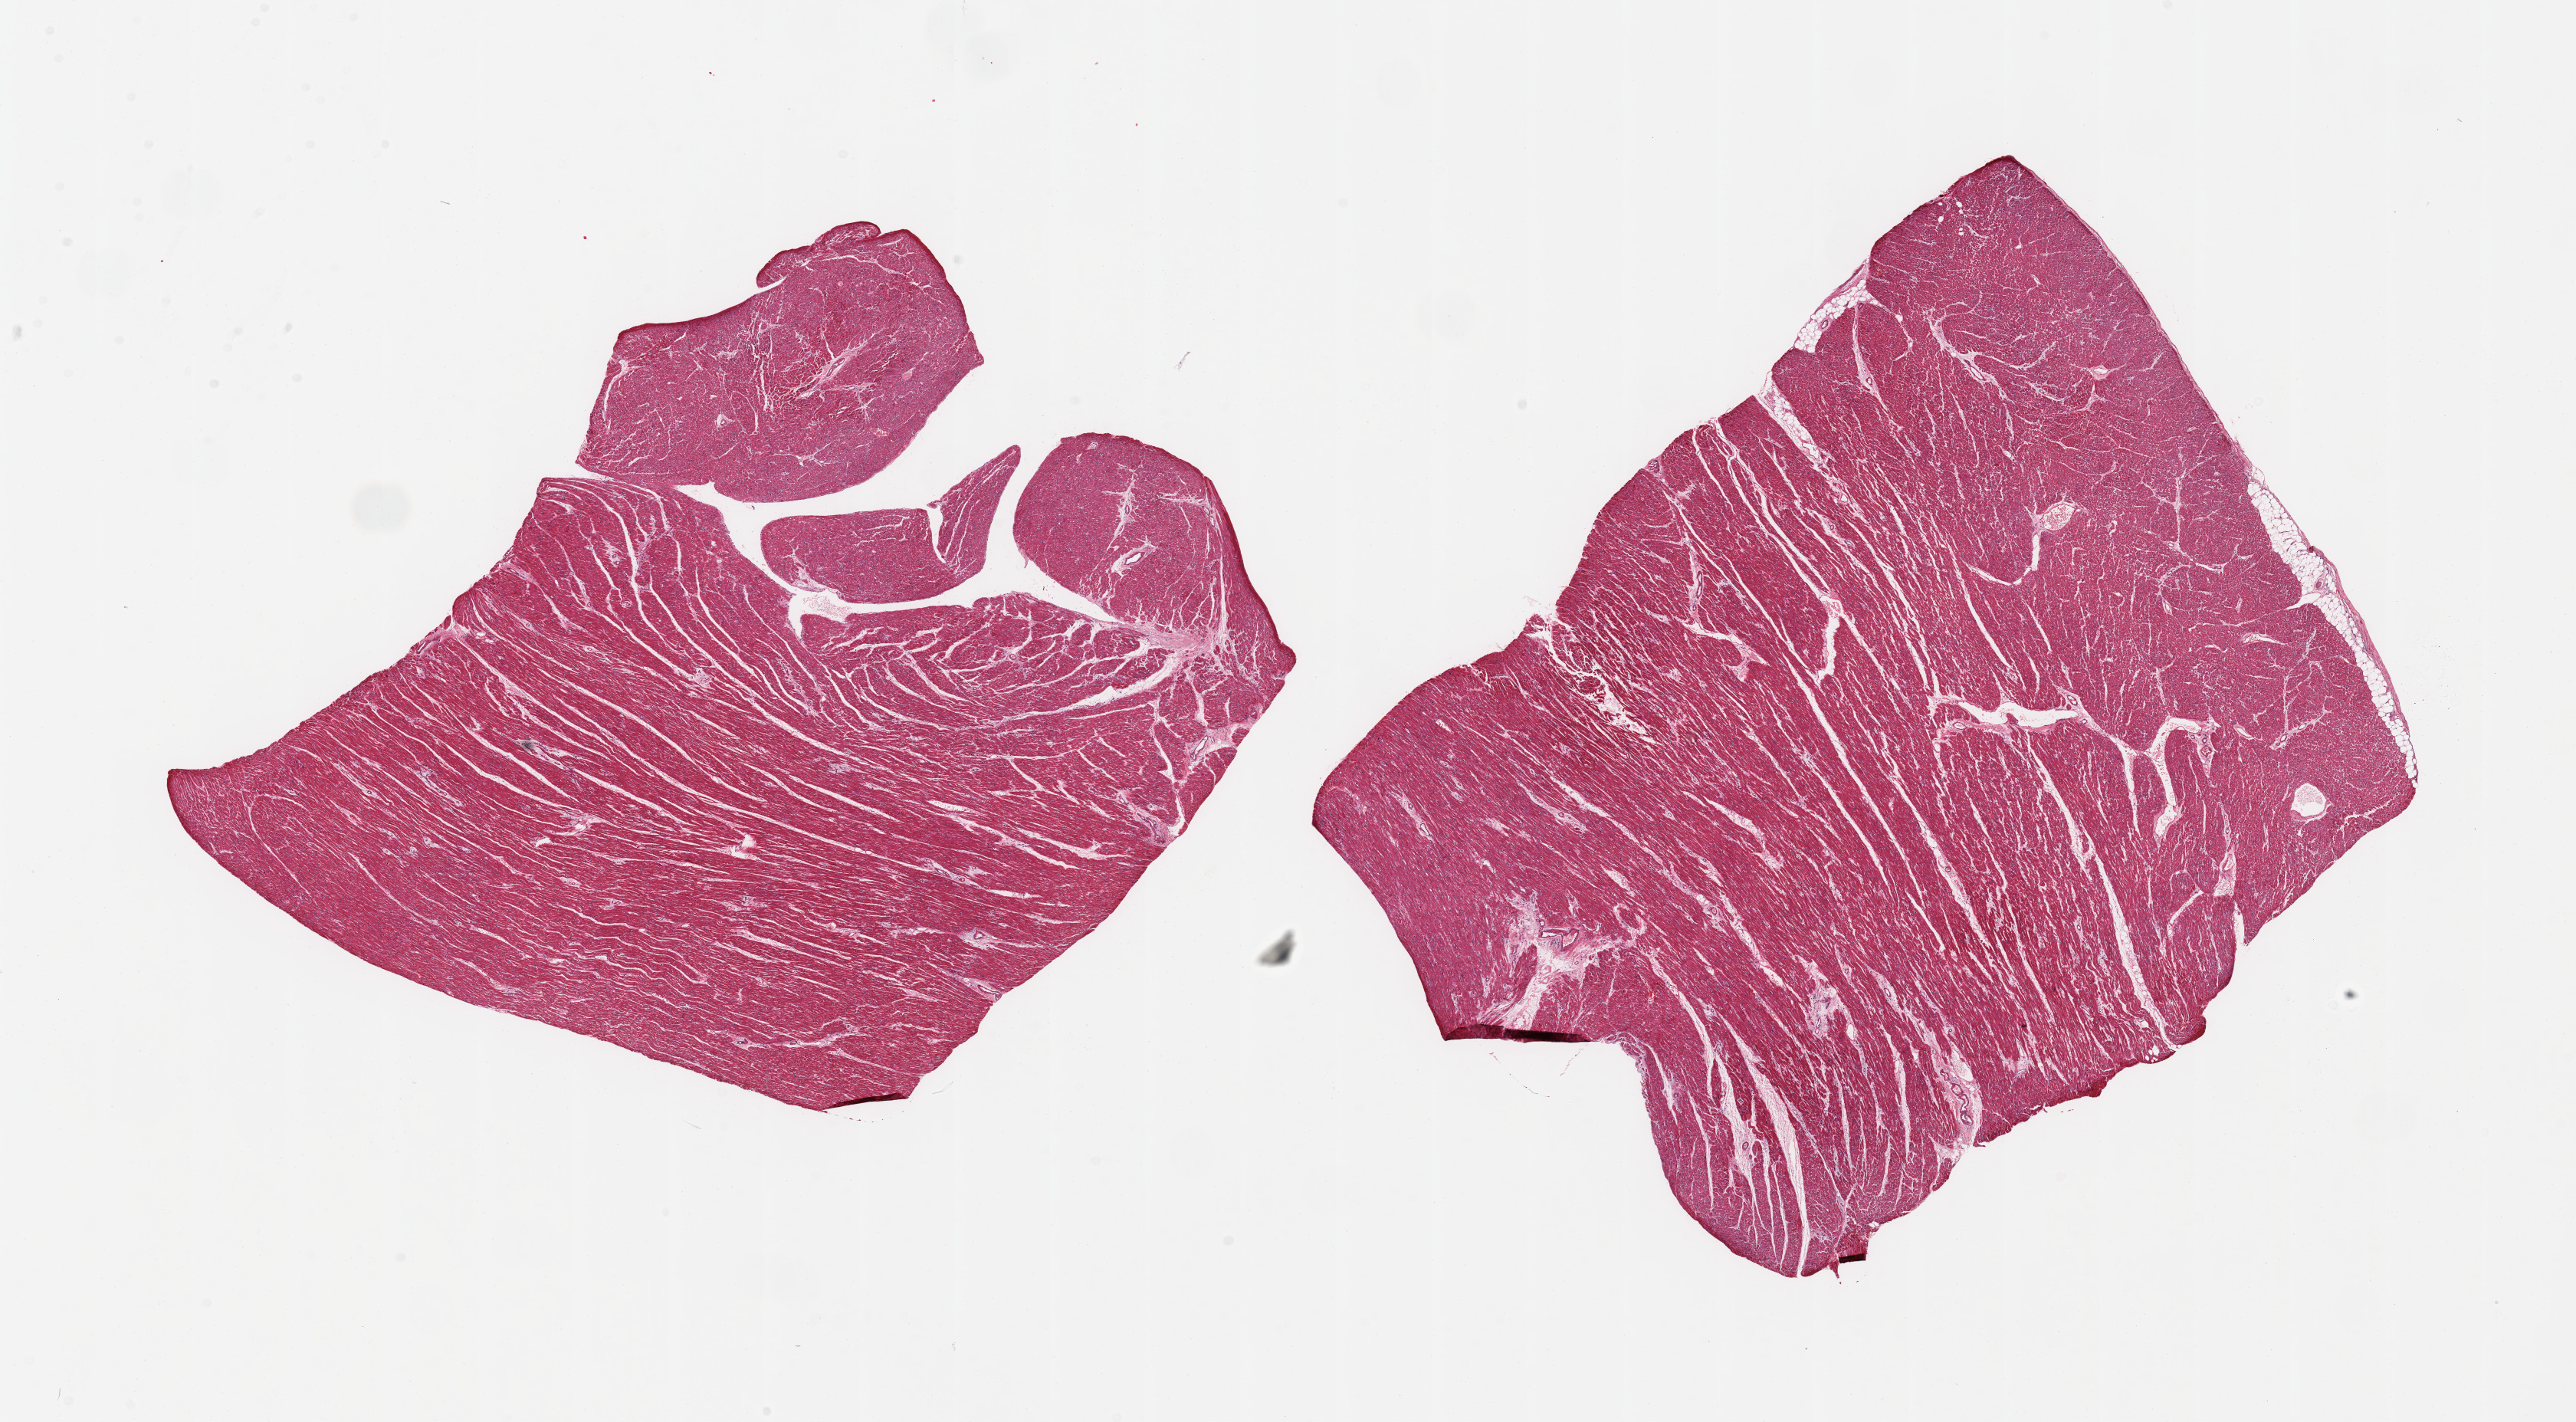
H&E whole-slide image, shown as a low-resolution overview of the whole scanned area (about 26.6 x 14.7 mm), PAXgene-fixed paraffin-embedded (PFPE) section, section of heart (target tissue), tissue donor sample. Donor: female.
Review note (as recorded): 2 pieces.